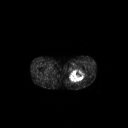
FDG PET of an extremity soft-tissue mass (from a PET/CT study), one axial slice; slice 256 of 267 in the series (ordered by position); 128 × 128 image matrix, field of view 700 × 700 mm. Patient: male, 44 years. From the clinical record (not read from this slice): histological type: undifferentiated pleomorphic liposarcoma; grade: high; site of the primary tumour: left thigh.
Structures marked on this image (expert contour drawn on MRI and transferred to this co-registered scan by the dataset authors):
- gross tumour volume including surrounding oedema: bounding box (x1, y1, x2, y2) in pixels: (68, 70, 84, 82)
- gross tumour volume (mass): (69, 71, 83, 82)